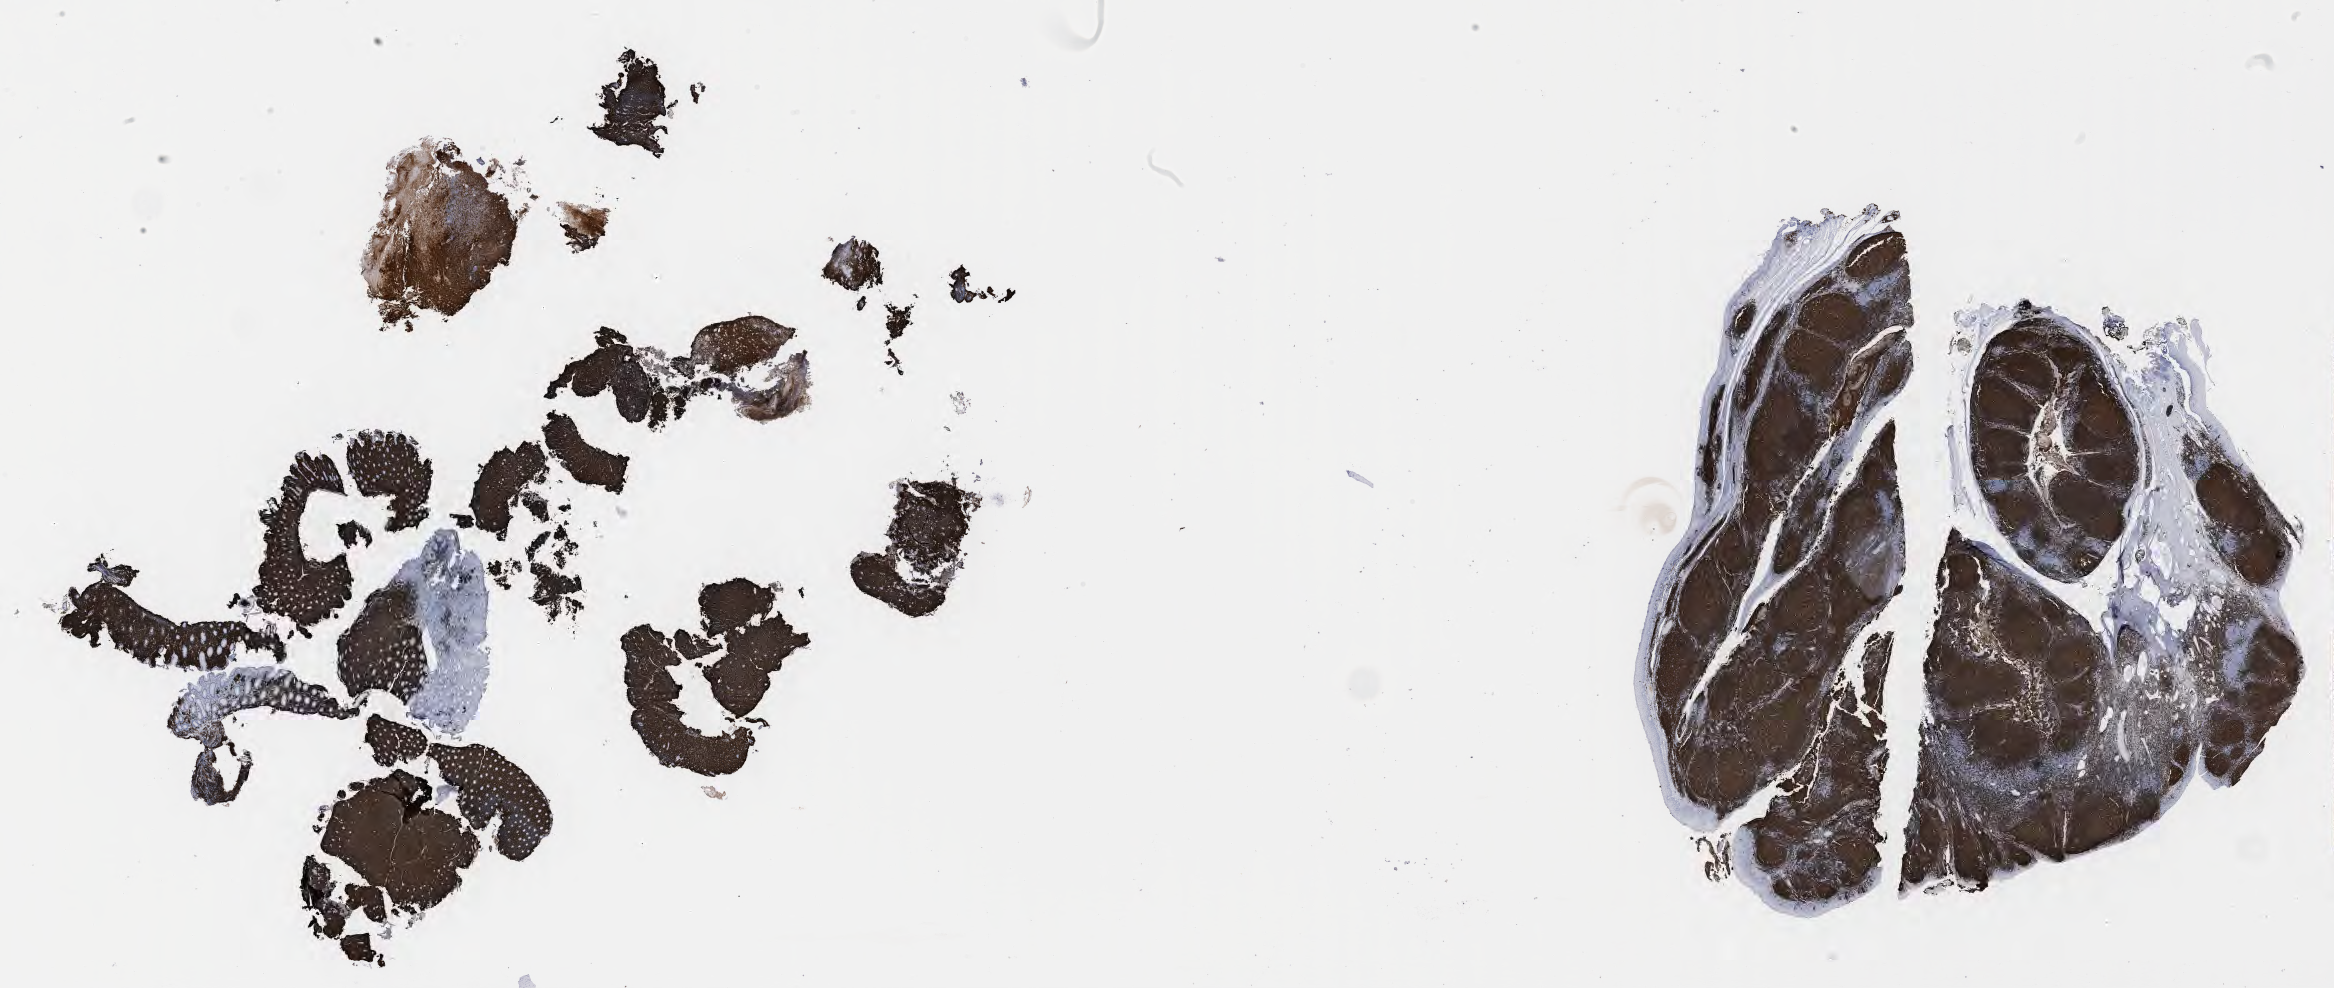
Immunohistochemistry (IHC) whole-slide image stained for CD20, low-resolution overview of the scanned area, about 37.7 x 16.0 mm. Specimen: tumor tissue. Male patient, 56 years old.
- histologic diagnosis: Burkitt lymphoma, NOS